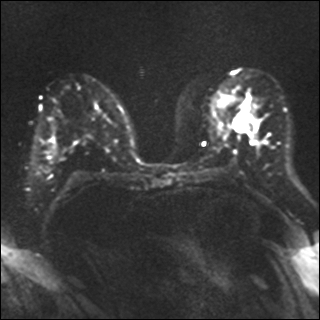
Breast MRI, one axial slice. Diffusion-weighted series; image 2 of 4 stored at this slice position (different b-values; order by instance number). 1.5 T. 4 mm slice thickness. 320 × 320 image matrix, field of view 320 × 320 mm. Female patient.
Structures marked on this image (expert manual segmentation):
- tumour on diffusion-weighted imaging: bounding box (x1, y1, x2, y2) in pixels: (233, 109, 254, 131)